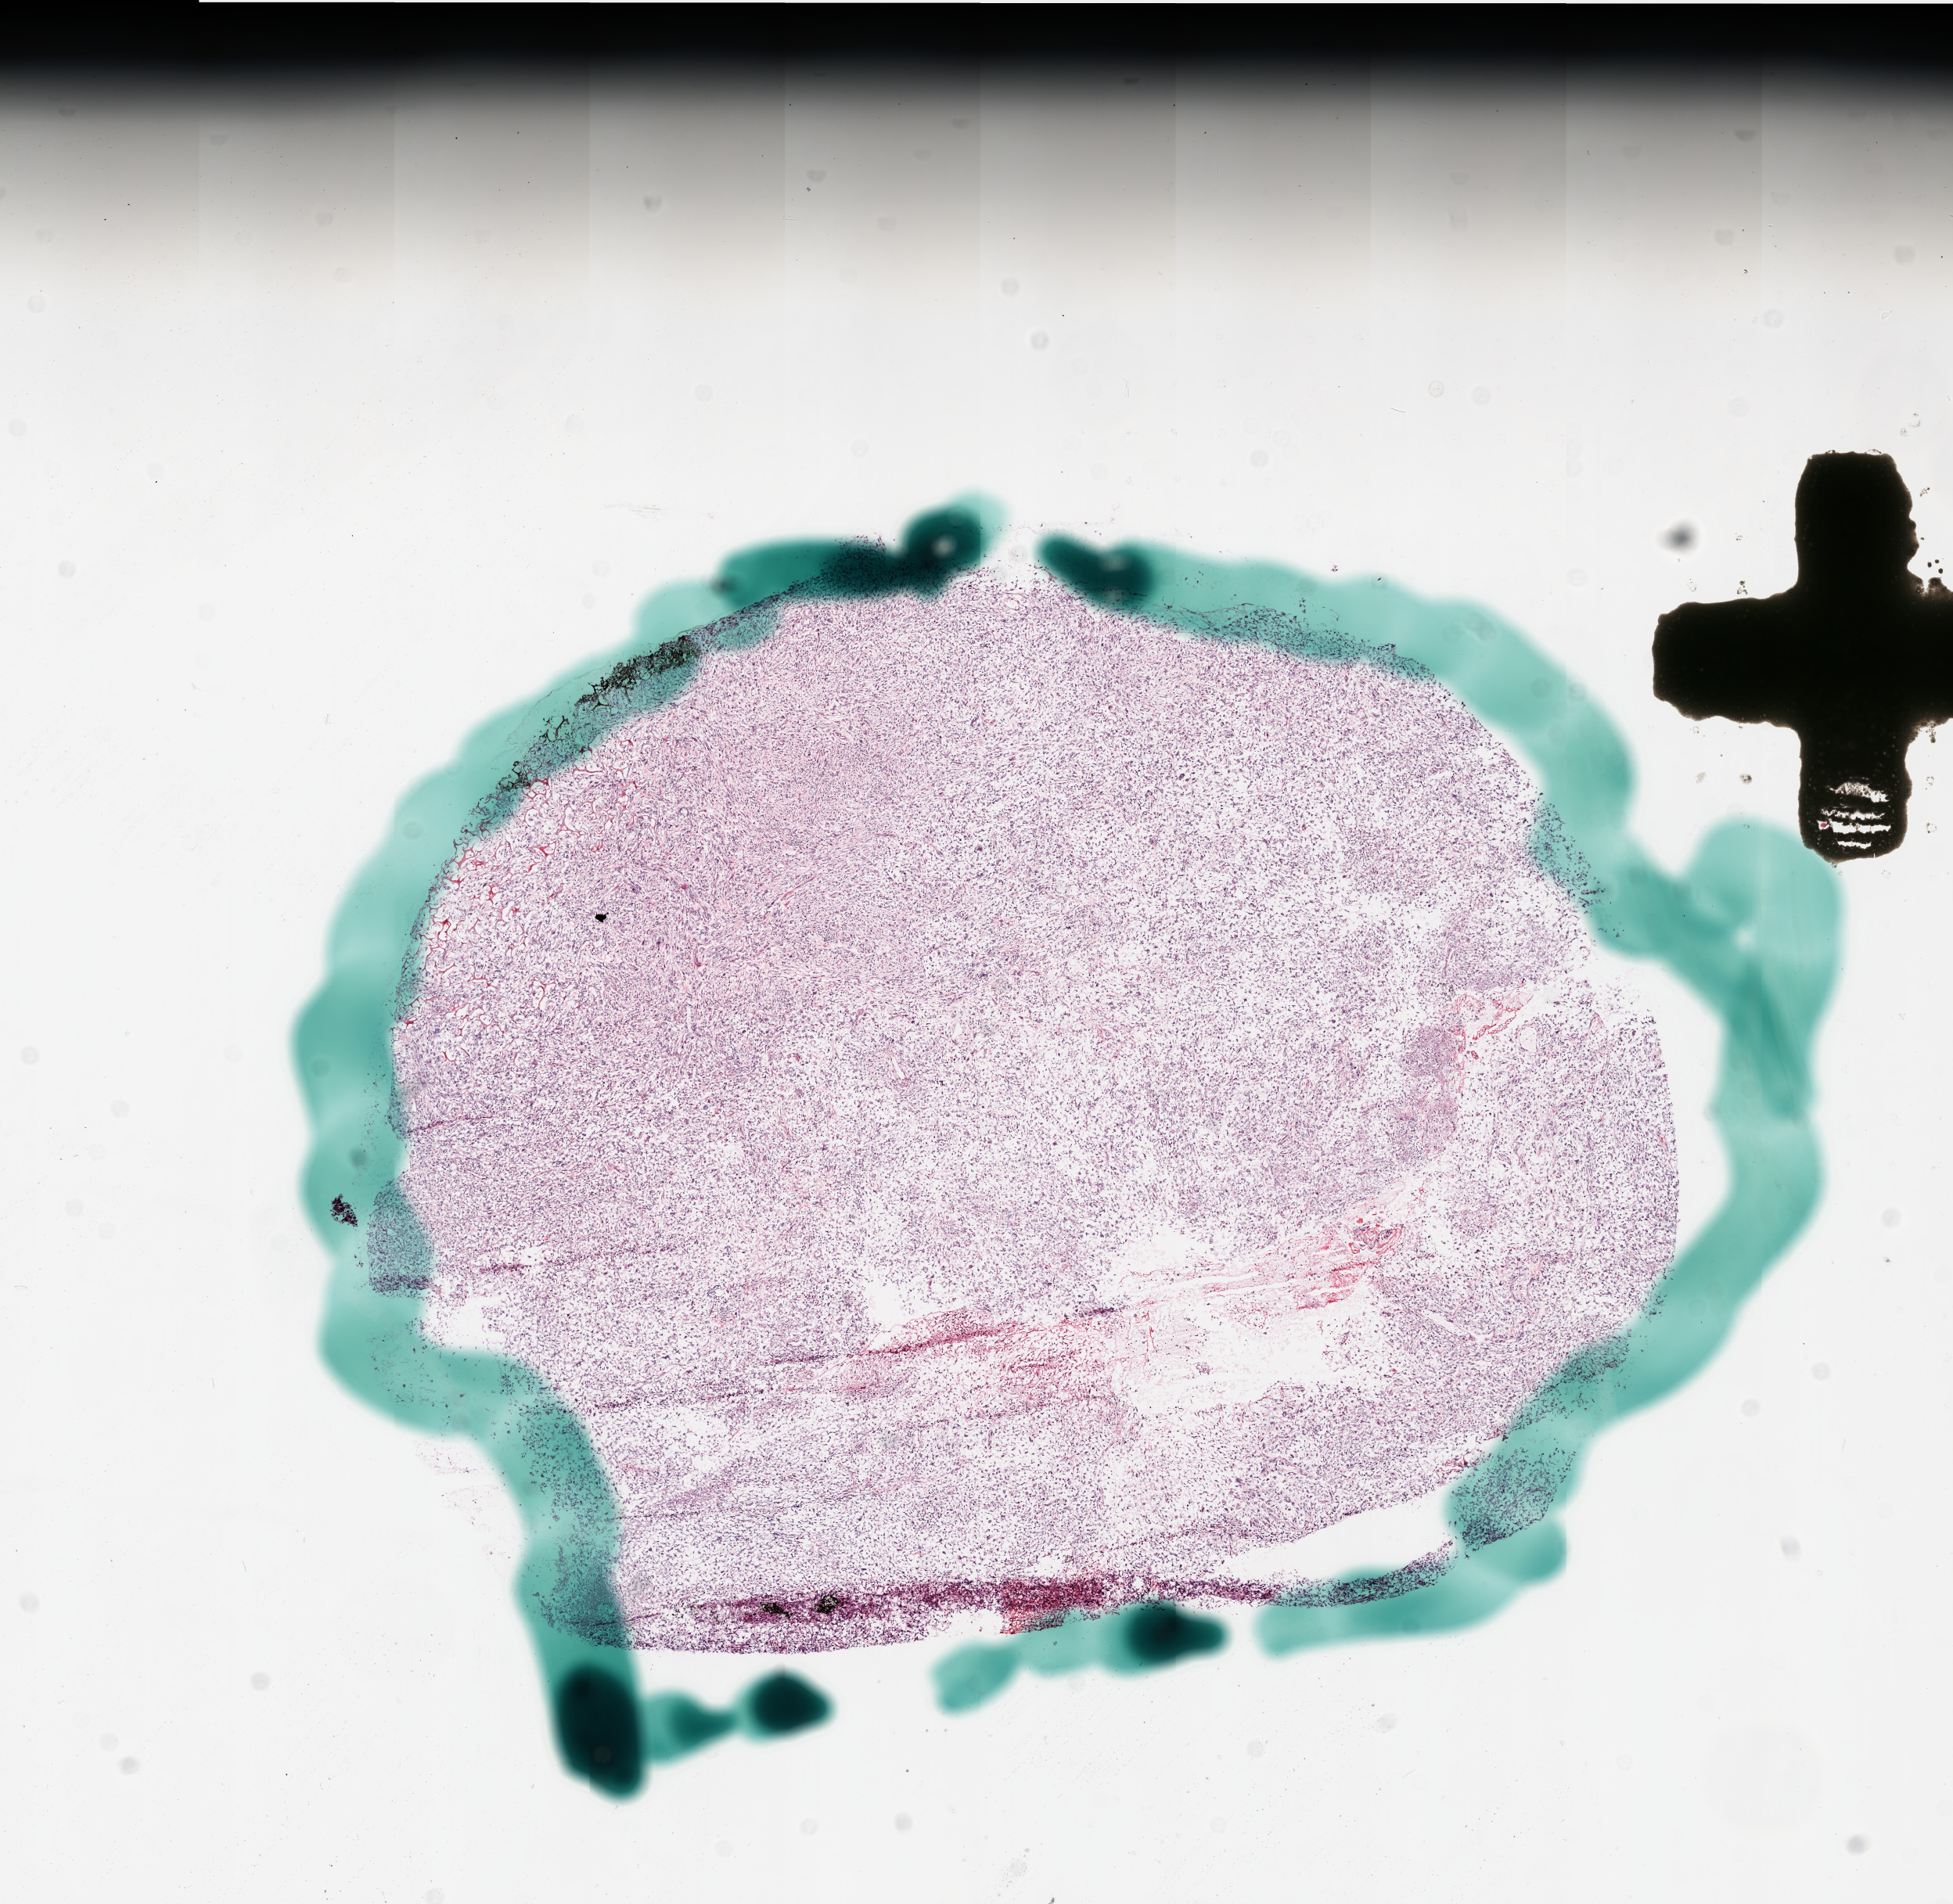
H&E whole-slide image, low-resolution overview of the scanned area, about 10.0 x 9.7 mm; frozen section from the bottom of the tissue portion; sample: primary tumour, brain. Male patient; age at initial diagnosis 54 years. Slide review estimates, as recorded: tumour cells 95%, tumour nuclei 95%, normal cells 0%, stromal cells 0%, necrosis 5%.
Diagnosis: Glioblastoma.